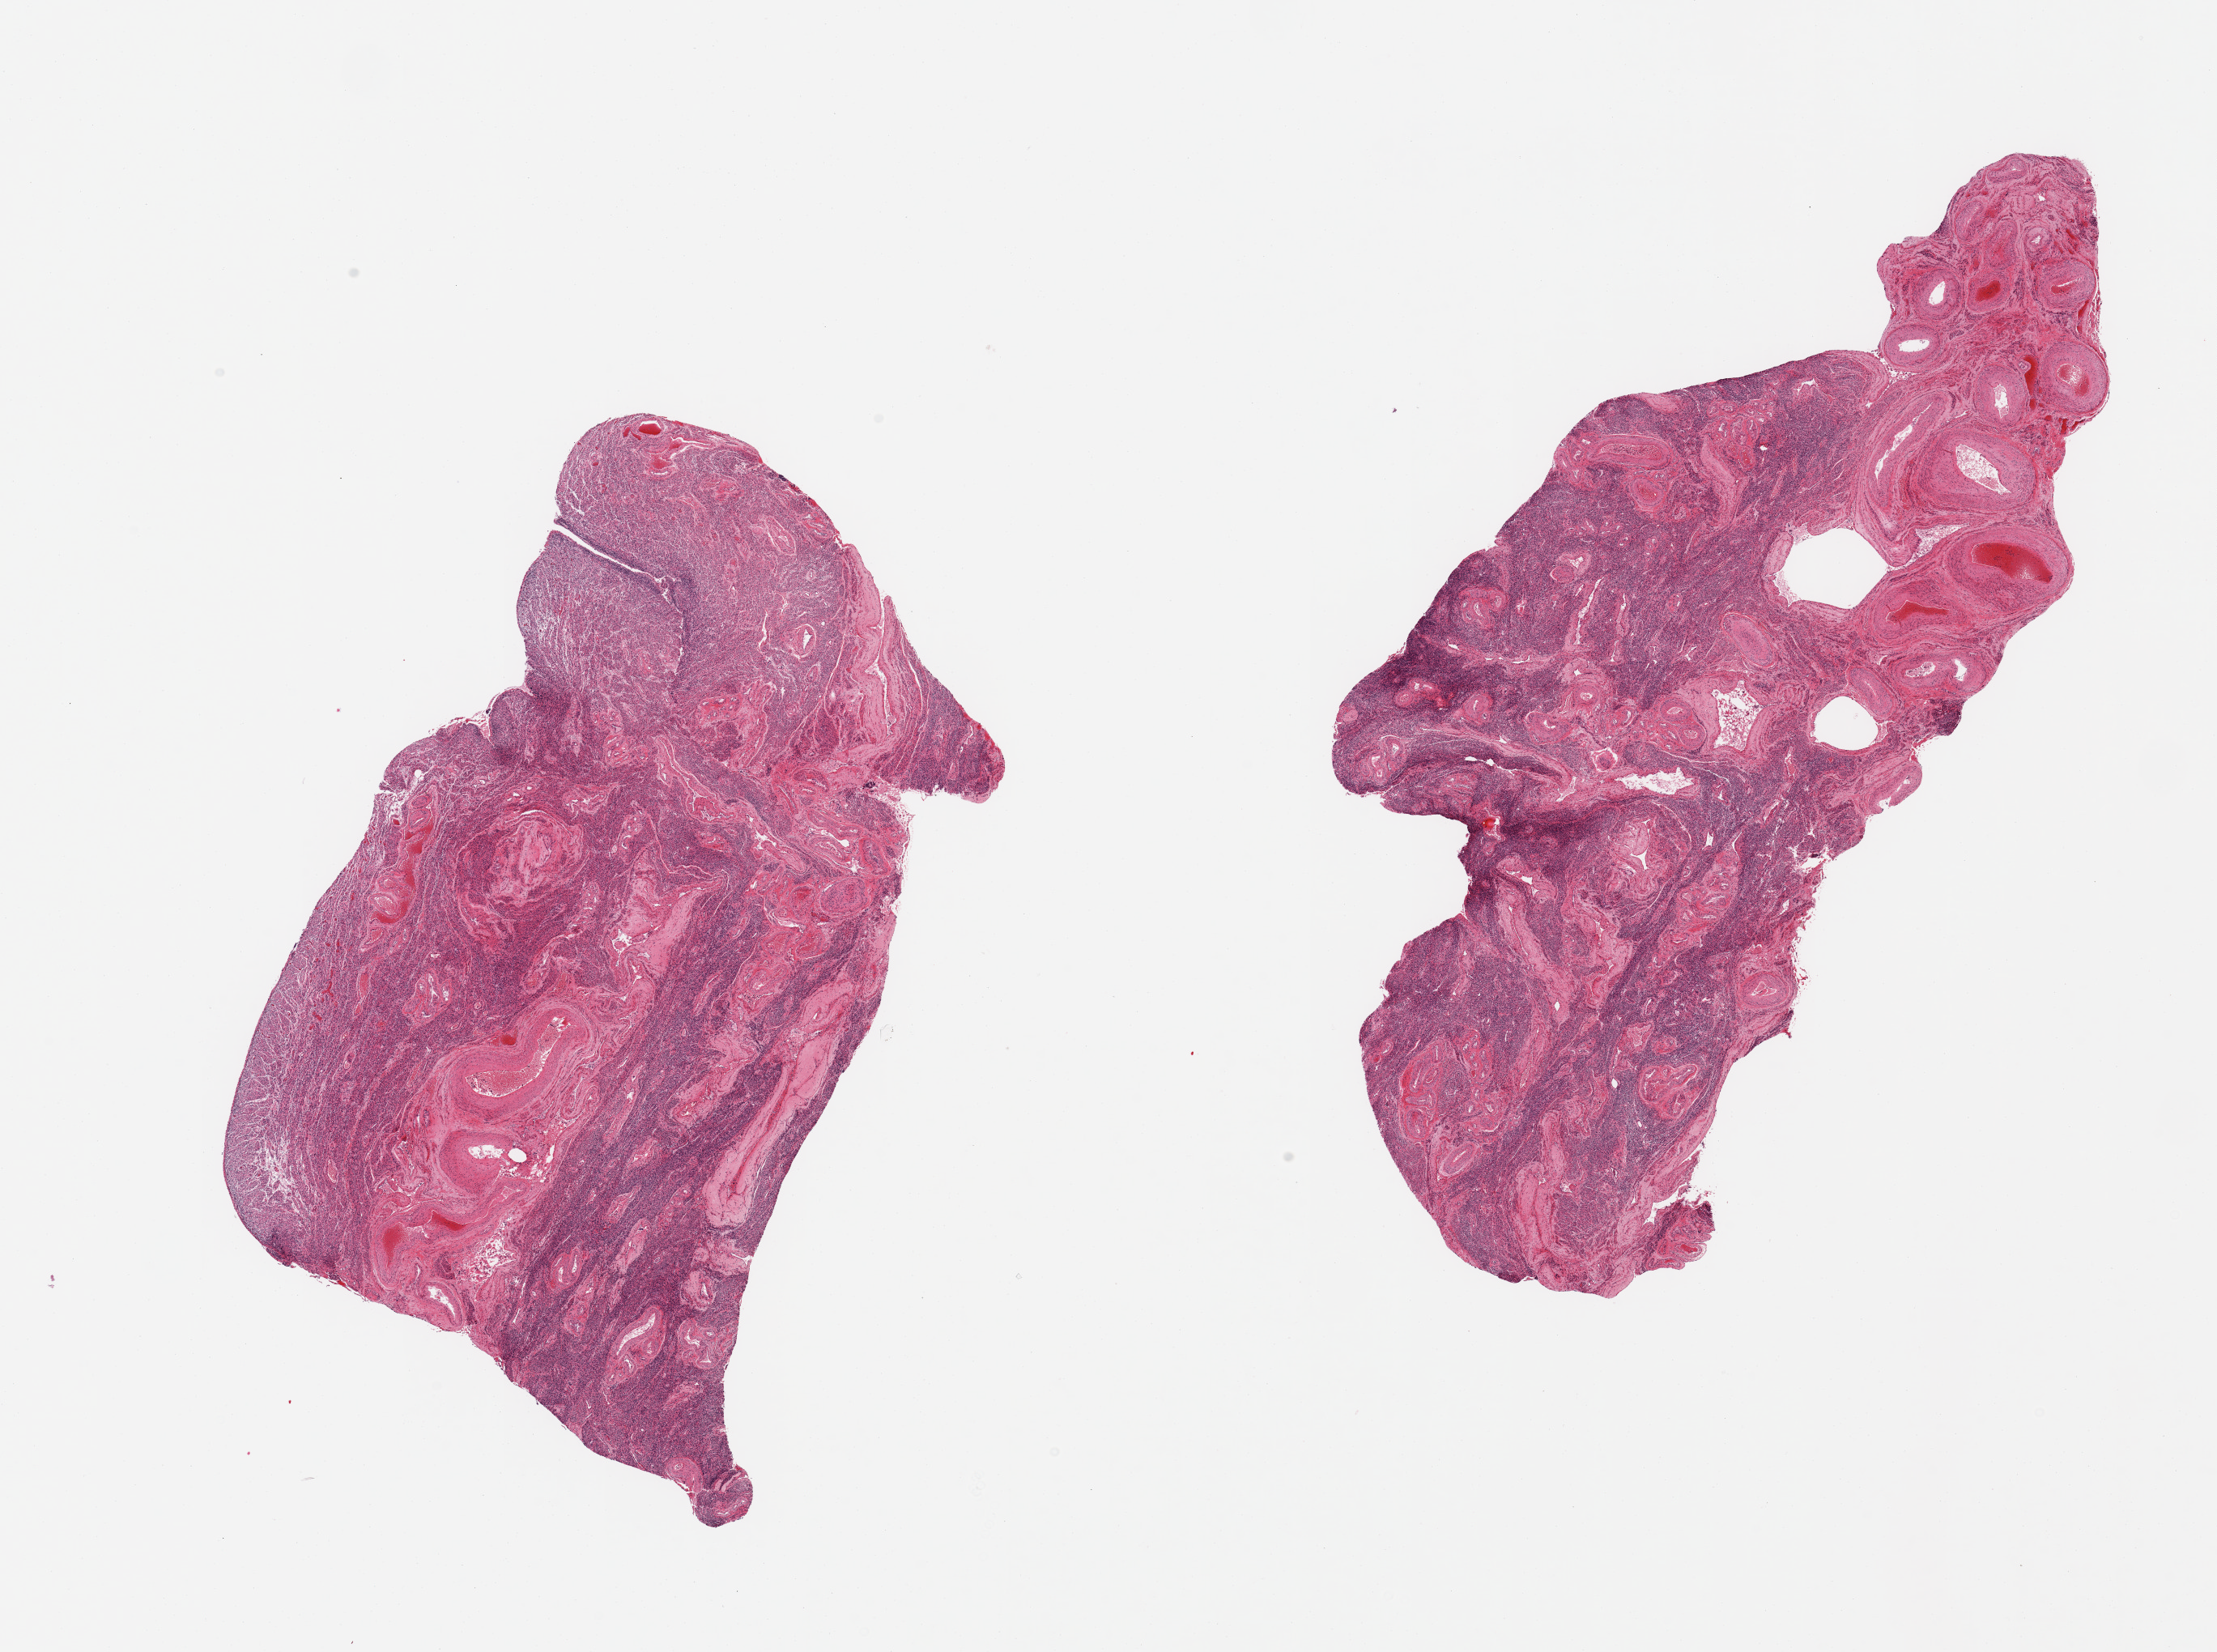
Whole-slide image, haematoxylin and eosin stain — shown as a low-resolution overview of the whole scanned area (about 21.7 x 16.1 mm); PAXgene-fixed paraffin-embedded (PFPE) section; section of uterus (target tissue); donor tissue sample. Donor sex: female.
- review note (as recorded): 2 pieces; all myometrium, no endometrium on these cuts